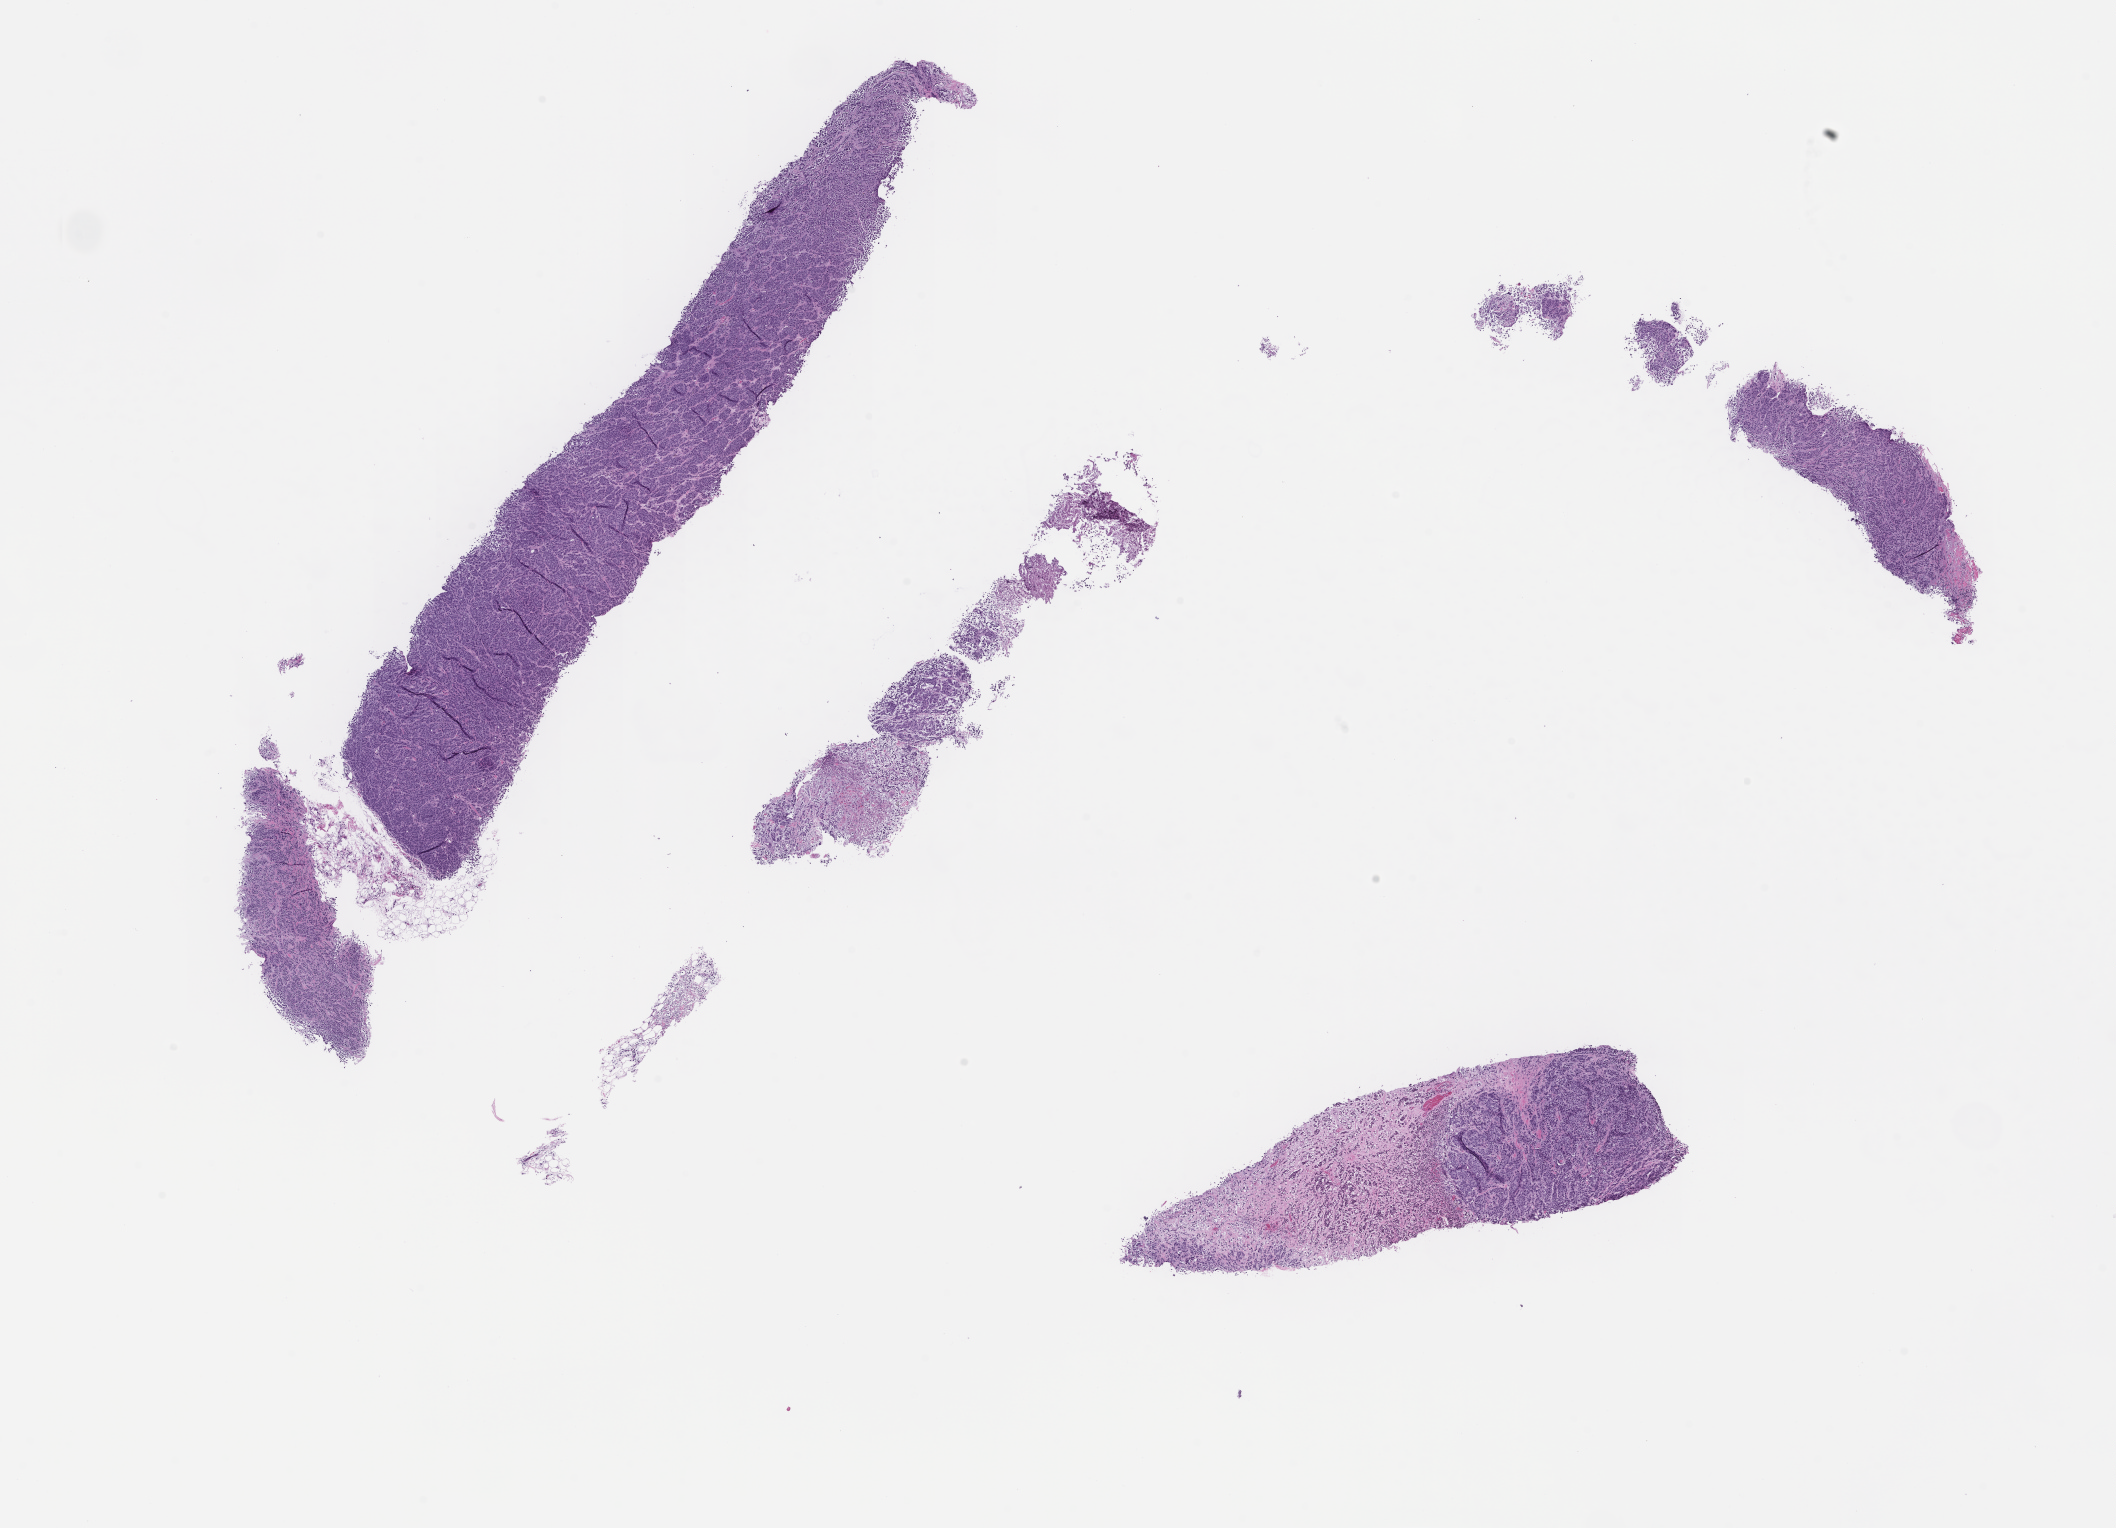
Haematoxylin and eosin whole-slide image, a low-resolution overview of the entire scanned area, about 17.1 x 12.3 mm, formalin-fixed paraffin-embedded section, specimen time point: collected at disease progression. Patient: female.
This section: metastasis (sampled organ not recorded). Patient diagnosis (primary): Melanoma.